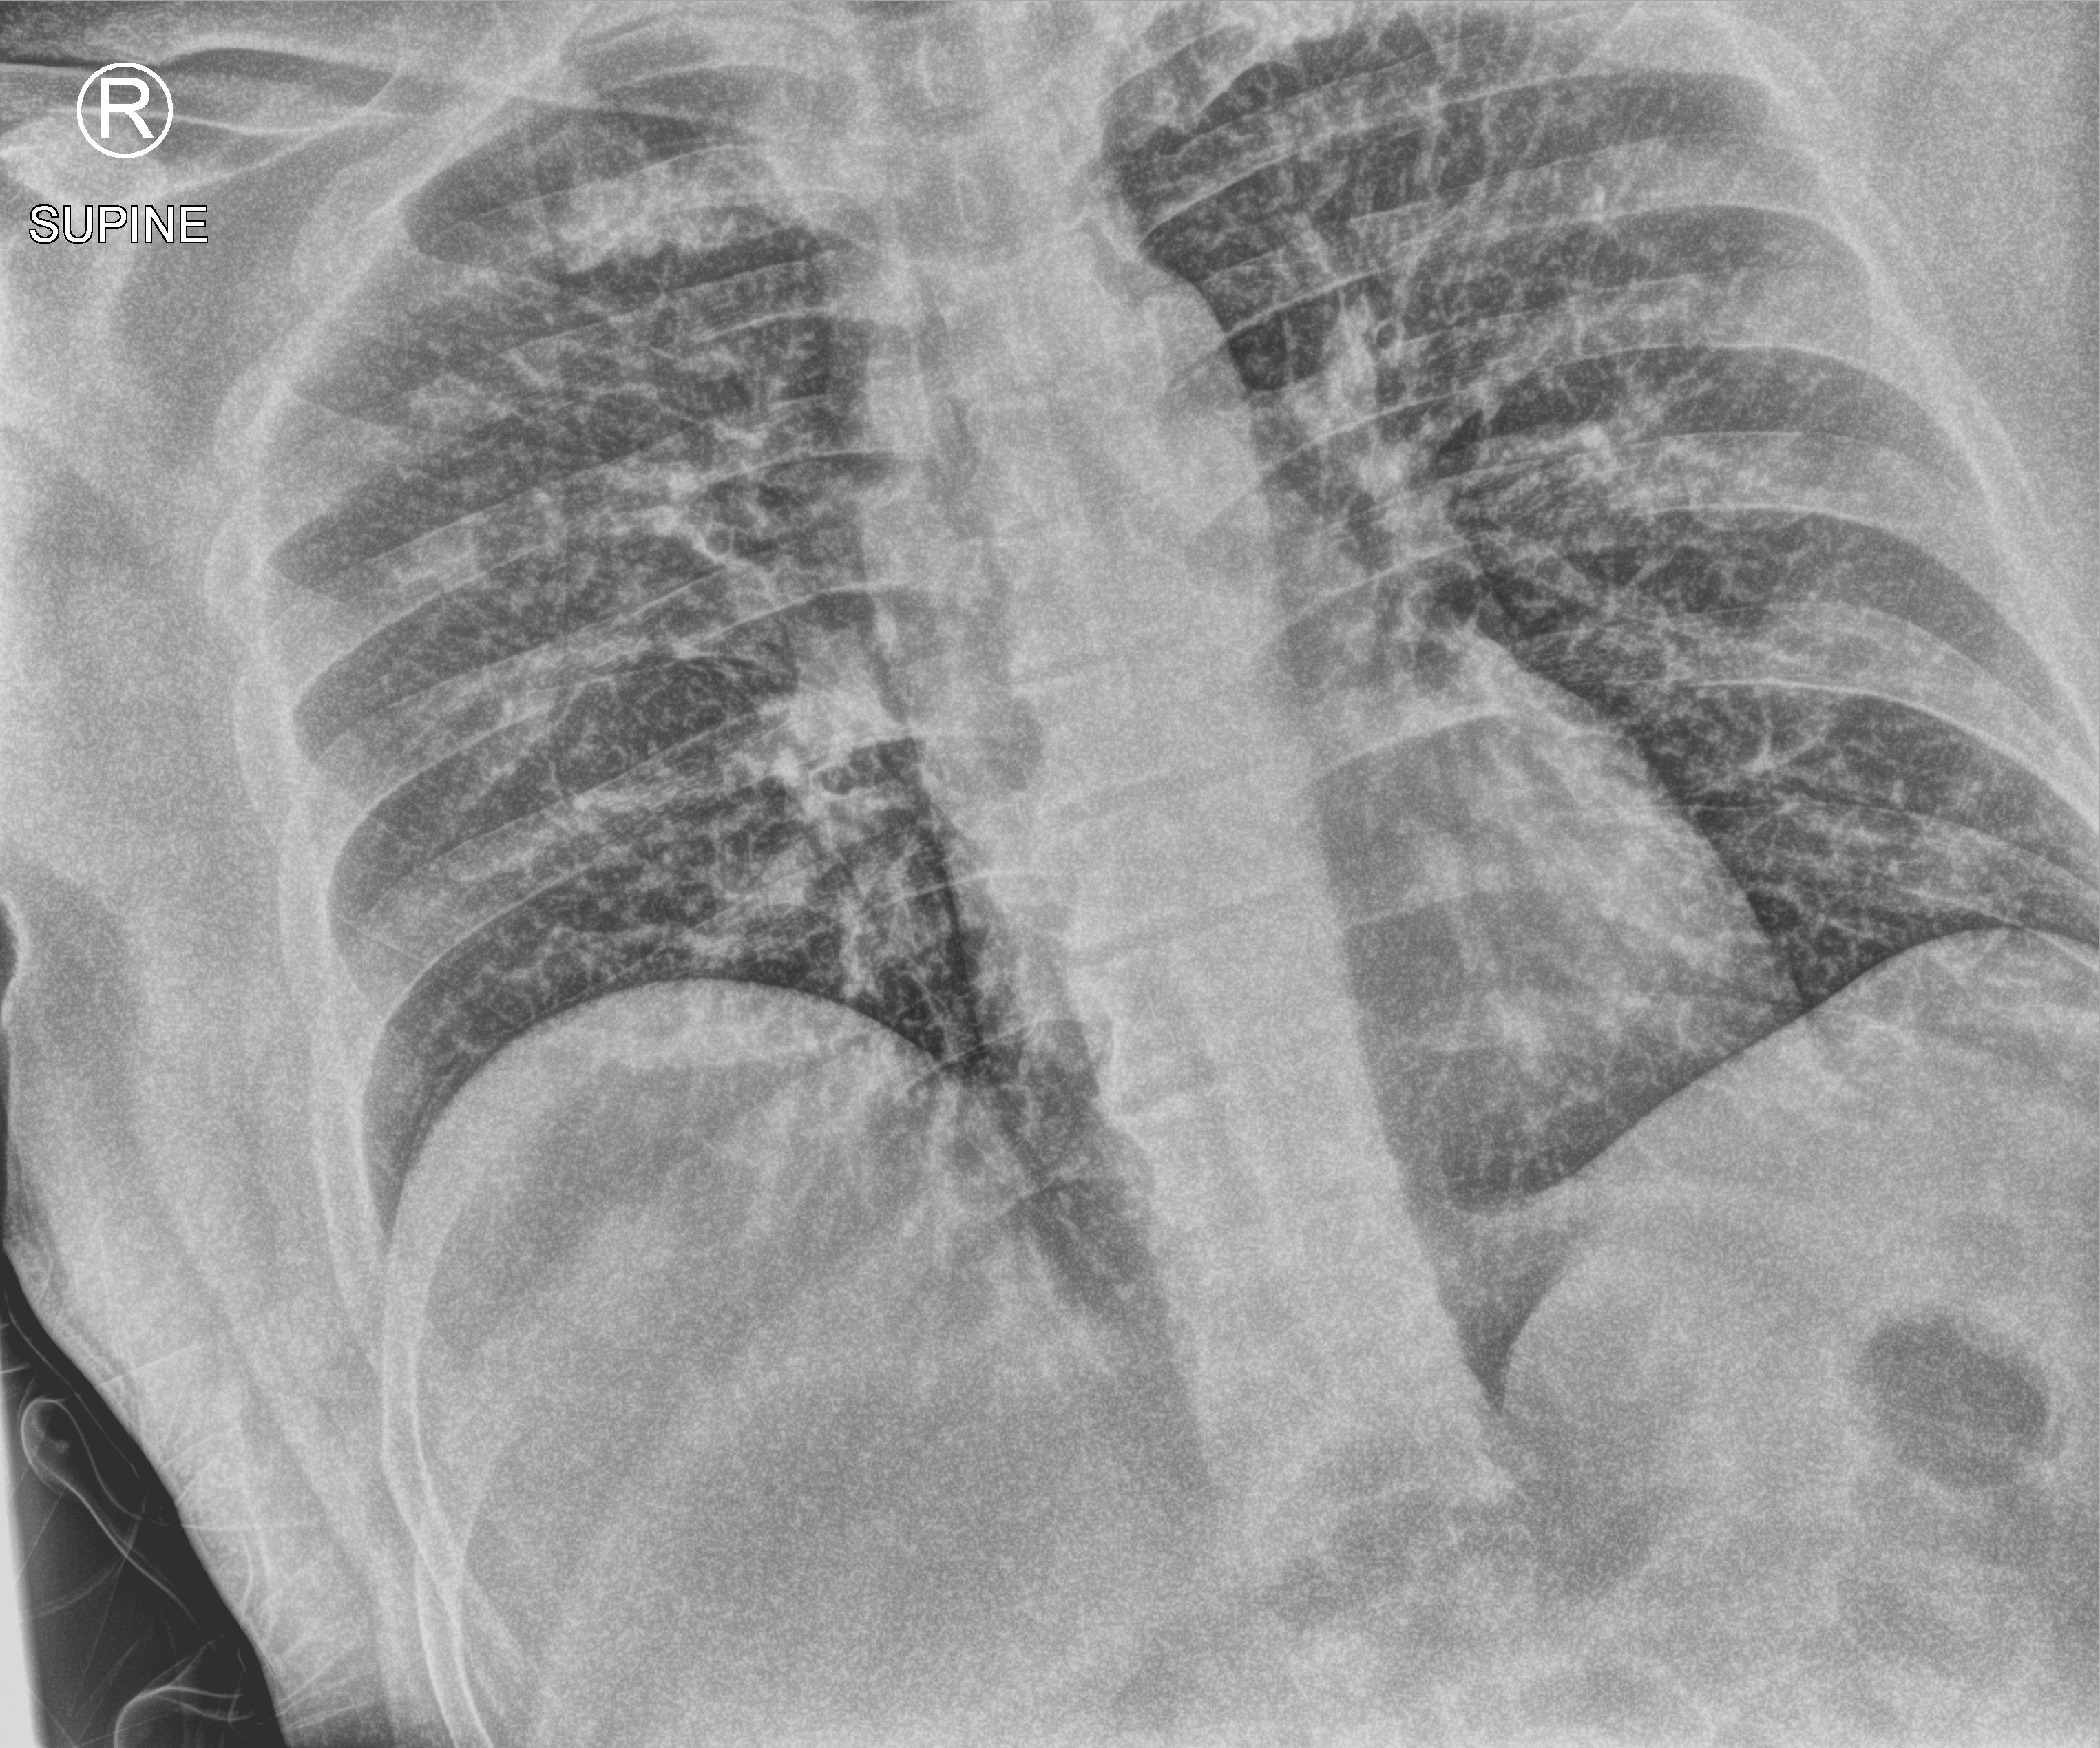
Bedside chest radiograph (computed radiography), anteroposterior (AP) projection. Patient hospitalised with COVID-19; male, aged 18–59 years.
Admission-level facts for this patient (not findings on this image; timing relative to this image not recorded): length of hospital stay: 2 days; mechanically ventilated during this hospital stay: no; admitted to intensive care during this hospital stay: no.